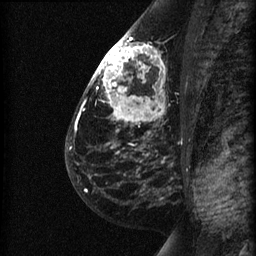
Breast MRI (dynamic contrast-enhanced), one sagittal slice; position 37 of 60 along the scan axis; dynamic contrast-enhanced series, image 2 of 3 at this slice position (ordered by acquisition); 1.5 T; TE 4.2 ms, TR 22.7 ms; 1.5 mm slice thickness; 256 × 256 image matrix. Female patient, age 48 years. Case-level facts recorded for this patient, not image findings: setting: breast cancer imaged before/during neoadjuvant chemotherapy; receptor status: triple-negative.
Outlined on this slice (semi-automatically segmented with operator editing):
- analysis volume of interest (the breast-tissue region the enhancement analysis was run in; not a lesion): bounding box (x1, y1, x2, y2) in pixels: (89, 27, 191, 178)
- tumour enhancement mask (voxels above the 90 % enhancement threshold inside the analysis volume of interest): (92, 34, 163, 108)